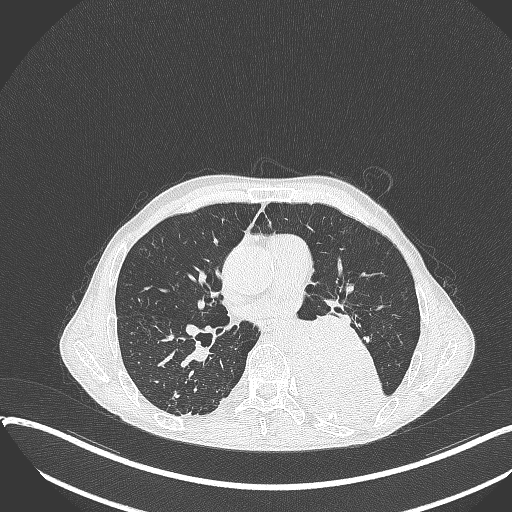
Chest CT, one axial slice; slice 192 of 401 in the series (ordered by position); 120 kVp; lung window (W 1500 / L -600 HU); 1 mm slice thickness; 512 × 512 image matrix, field of view 400 × 400 mm. Patient: male, 57 years. Case-level facts recorded for this patient, not image findings: clinical TNM (as recorded): T4 N0 M0.
Structures marked on this image (rectangle marked by the reading radiologist):
- lung tumour (recorded histology: squamous cell carcinoma): bounding box [x1, y1, x2, y2] px = [281, 313, 387, 423]